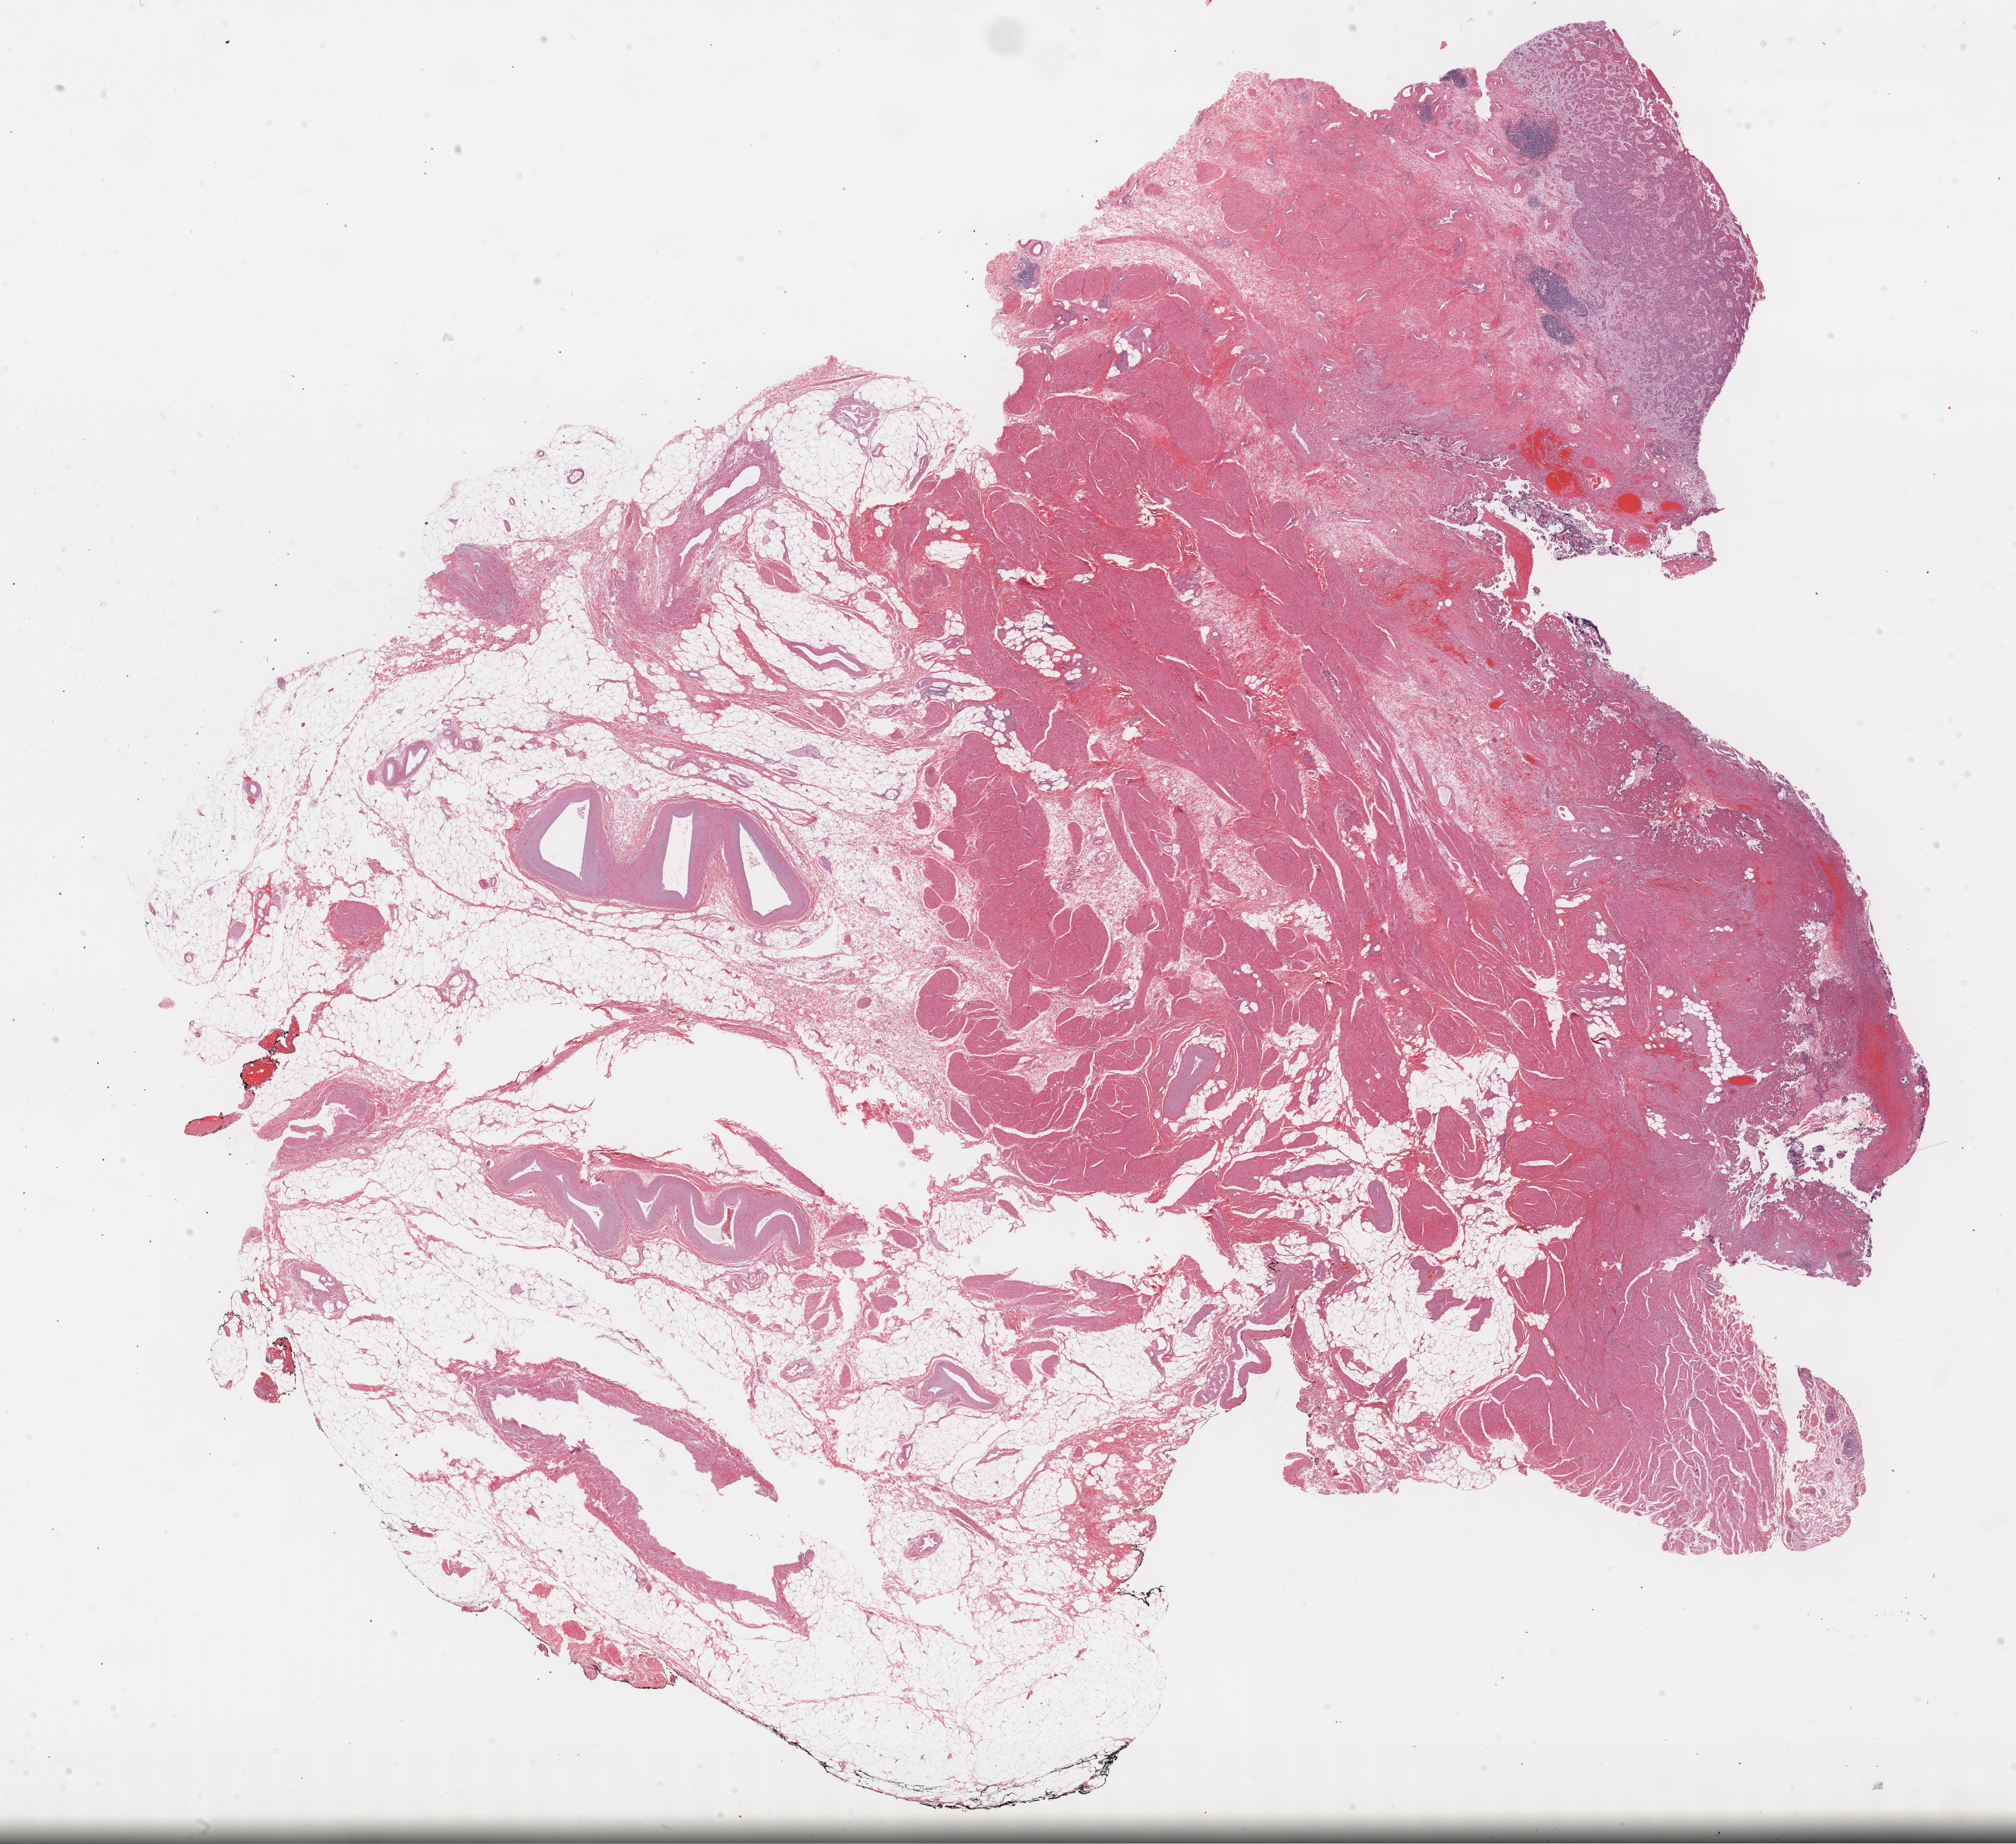
Digitized H&E tissue section (whole slide) — low-resolution overview of the scanned area, about 25.2 x 23.0 mm (slide scanned at 40x); formalin-fixed paraffin-embedded (FFPE) diagnostic section; sample: primary tumour, bladder. Female, age 74 years at initial diagnosis. Histologic grade: high grade.
AJCC pathologic stage: IV (6th edition). Diagnosis: Papillary transitional cell carcinoma.